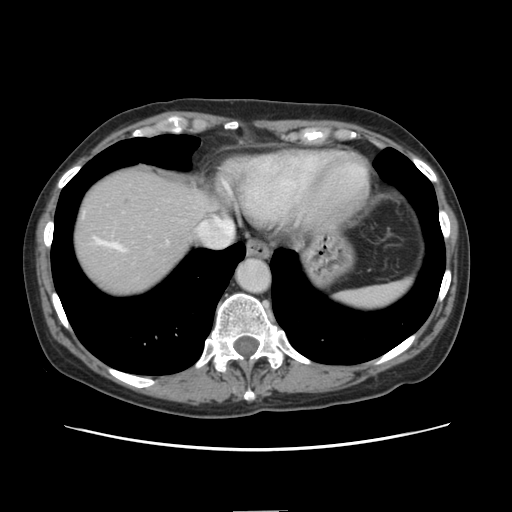
Contrast-enhanced abdominal CT, one axial slice. Position 125 of 141 along the scan axis. 120 kVp. Intravenous contrast given. Soft-tissue window (W 400 / L 40 HU). 2.5 mm slice thickness. 512 × 512 image matrix. Female patient, age 63 years. From the clinical record (not read from this slice): diagnosis: colorectal cancer liver metastases, imaged before liver resection; multiple liver metastases: yes; largest metastasis: 3.2 cm; disease in both lobes: yes.
Annotated regions visible in this slice (manually delineated by an expert):
- hepatic veins: bounding box <96,219,224,249> (left, top, right, bottom; pixels)
- liver: <74,164,223,297>
- planned liver remnant (the part of the liver to remain after resection): <212,203,223,220>